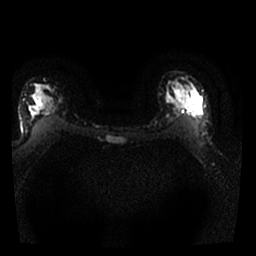
Breast MRI, one axial slice. Diffusion-weighted series; image 2 of 4 stored at this slice position (different b-values; order by instance number). 1.5 T. 4 mm slice thickness. 256 × 256 image matrix. Female patient.
Structures marked on this image (expert manual segmentation):
- tumour on diffusion-weighted imaging: bounding box (x1, y1, x2, y2) in pixels: (163, 87, 171, 102)